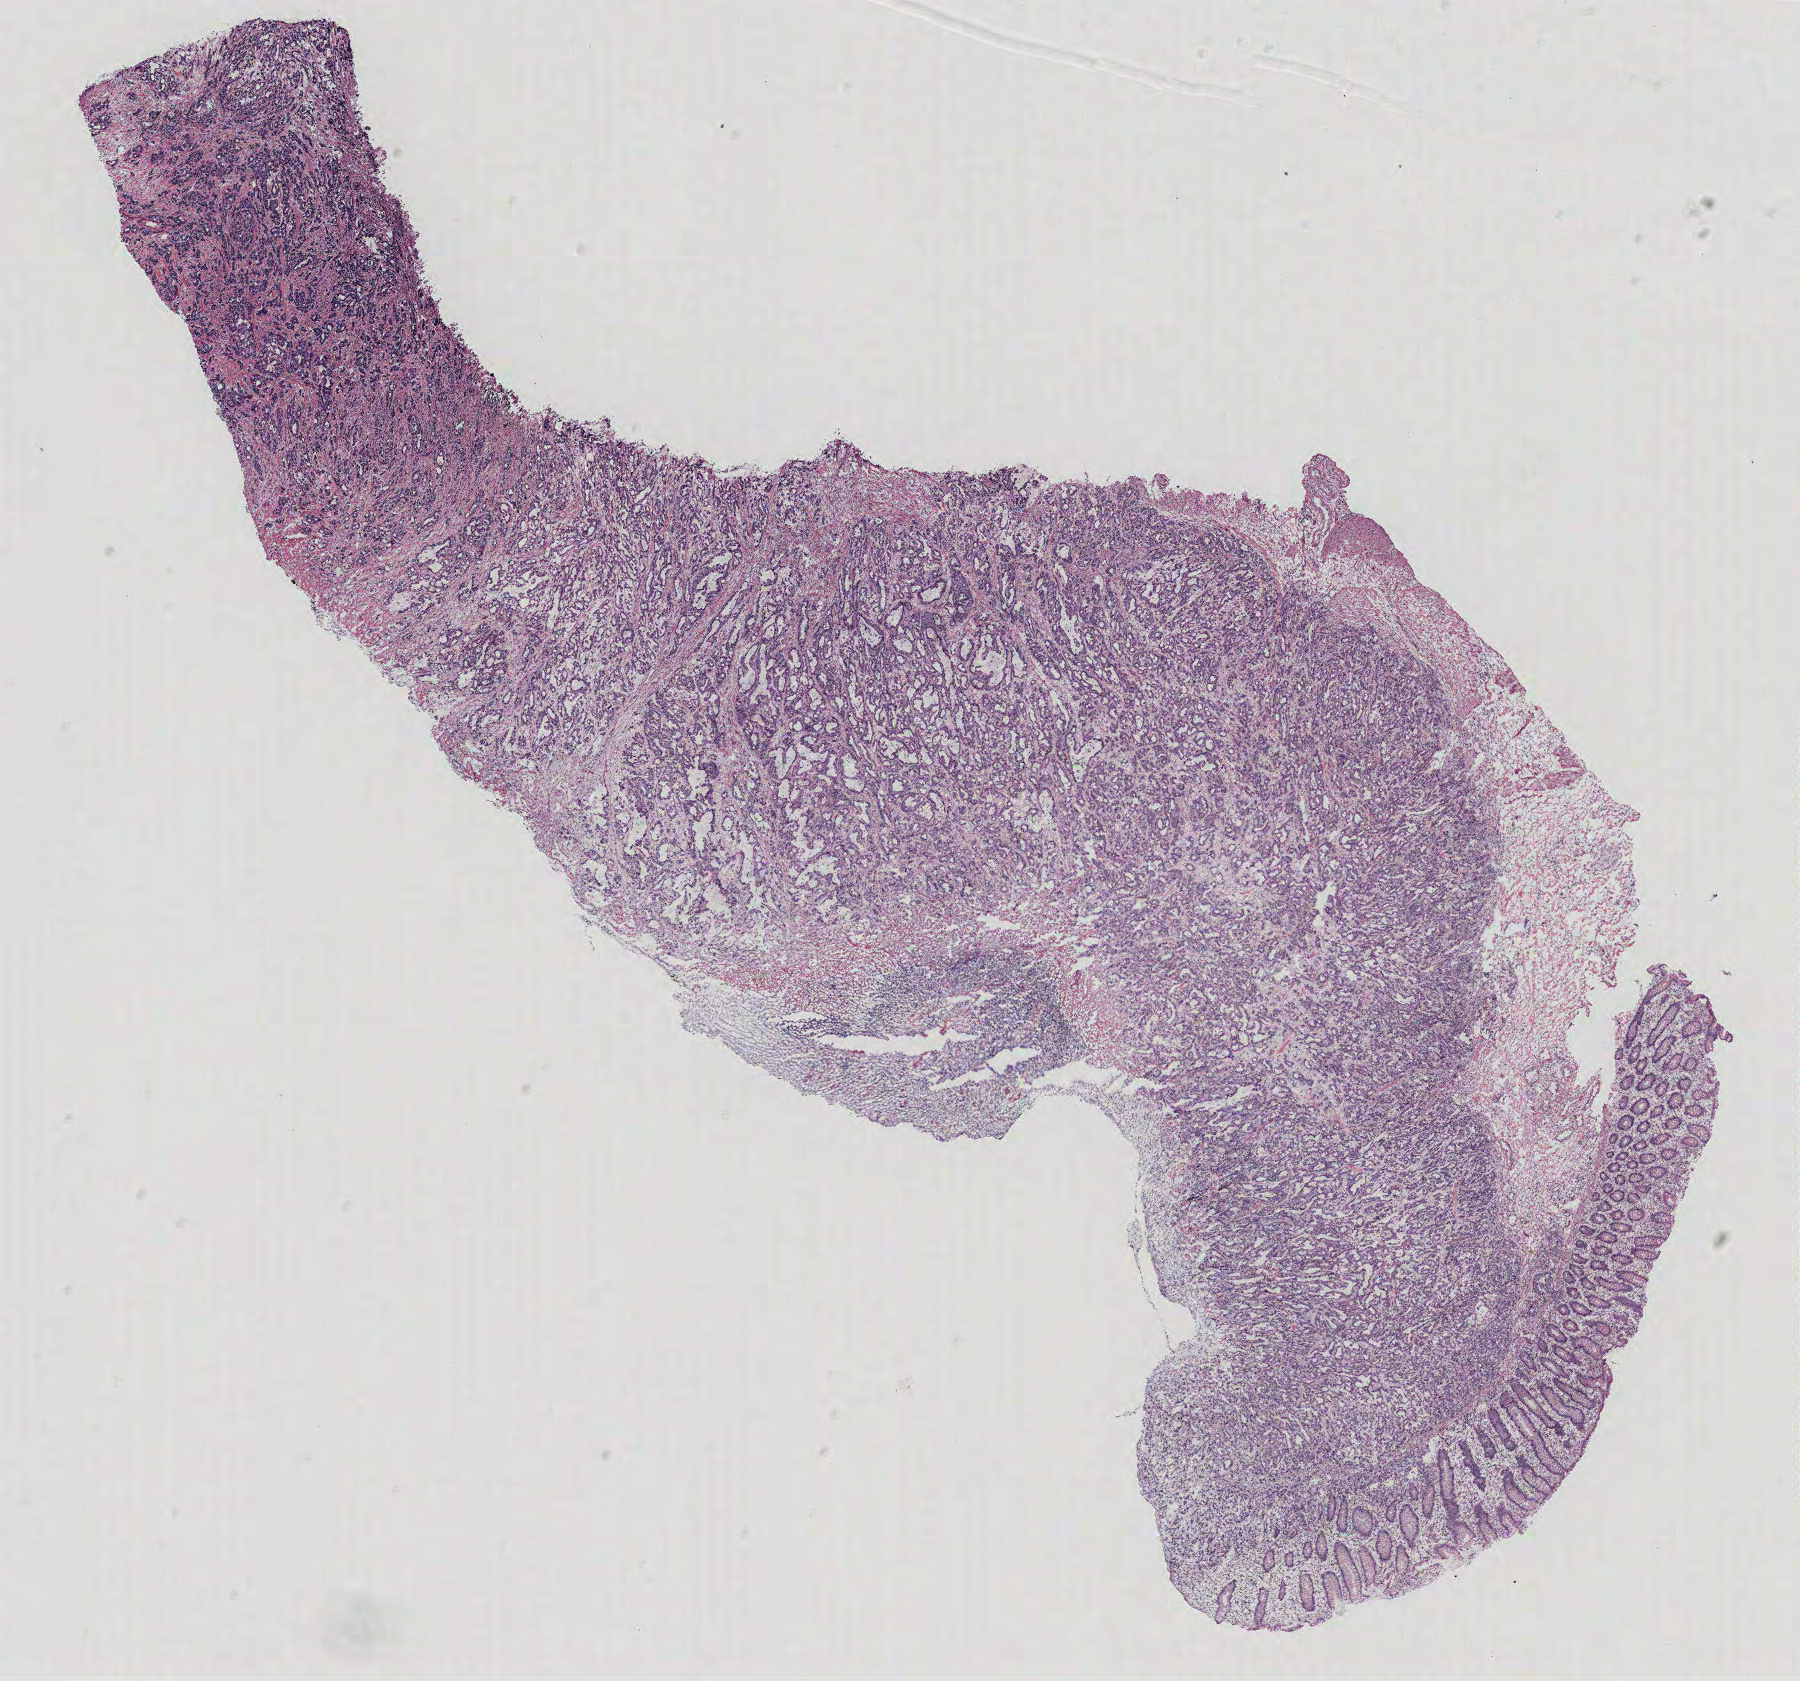
H&E whole-slide image — whole scanned area (about 14.4 x 13.5 mm, acquisition: 40x scan) shown as a low-resolution overview. Tumour tissue sample, colon. Female, 78 y/o.
Diagnosis: Adenocarcinoma, NOS.